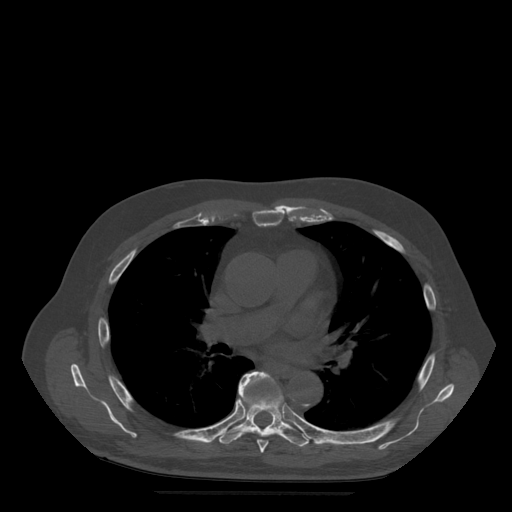
CT including the spine, one axial slice. Slice 341 of 522 in the series (ordered by position). Bone window (W 1800 / L 400 HU). 1.25 mm slice thickness. 512 × 512 image matrix, field of view 420 × 420 mm. Patient age 72 years. From the clinical record (not read from this slice): primary cancer: prostate.
Structures marked on this image (semi-automatically segmented with operator editing):
- T6 vertebra: box from (x=239, y=372) to (x=276, y=453) px
- T7 vertebra: (x=216, y=381)–(x=311, y=448)